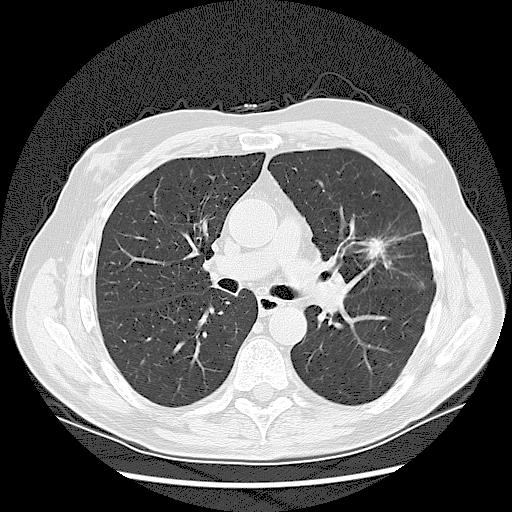
Low-dose screening chest CT, one axial slice; slice 78 of 132 in the series (ordered by position); 120 kVp; lung window (W 1500 / L -600 HU); 512 × 512 image matrix, field of view 380 × 380 mm.
Annotated regions visible in this slice (expert manual segmentation):
- lesion 1 (tumor, upper lobe of left lung): bounding box <369,238,385,258> (left, top, right, bottom; pixels)